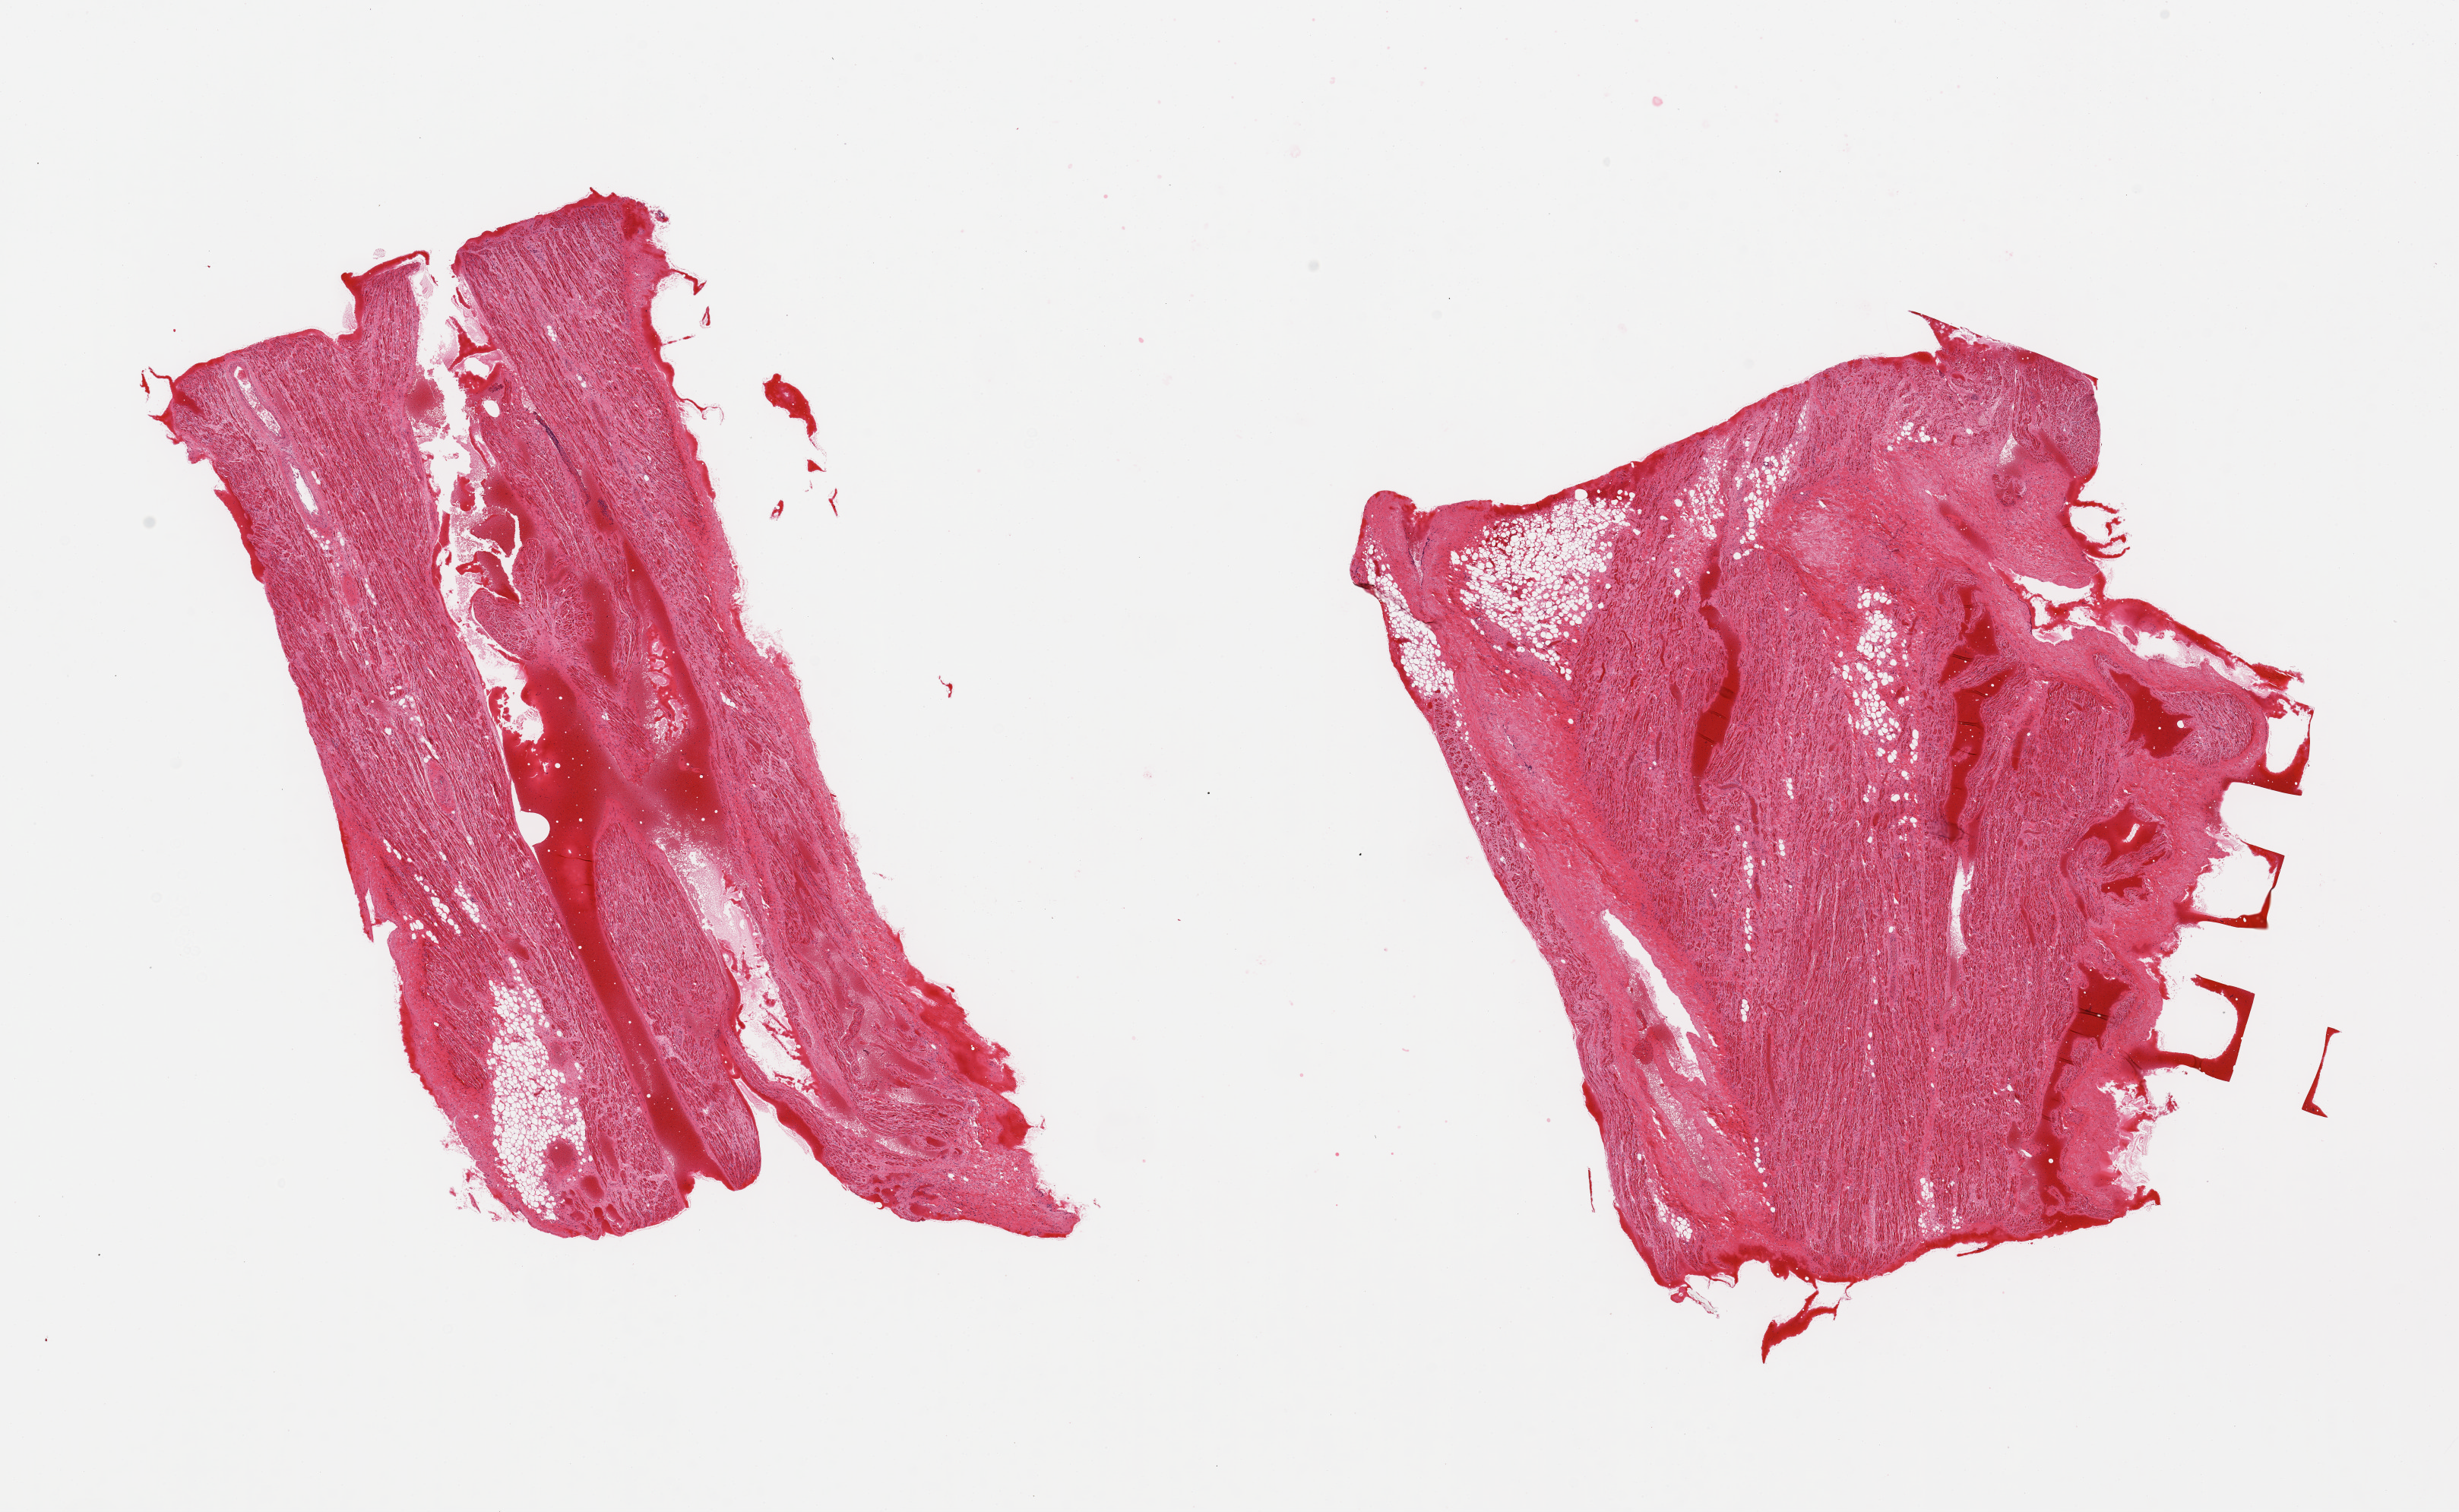
Digitized haematoxylin and eosin-stained section, a low-resolution overview of the entire scanned area, about 25.6 x 15.7 mm (acquisition: 20x scan). PAXgene-fixed paraffin-embedded (PFPE) section. Target tissue: auricular appendage. Tissue donor sample. Male donor.
Reviewer comment on this tissue sample: 2 pieces, unusually congested.